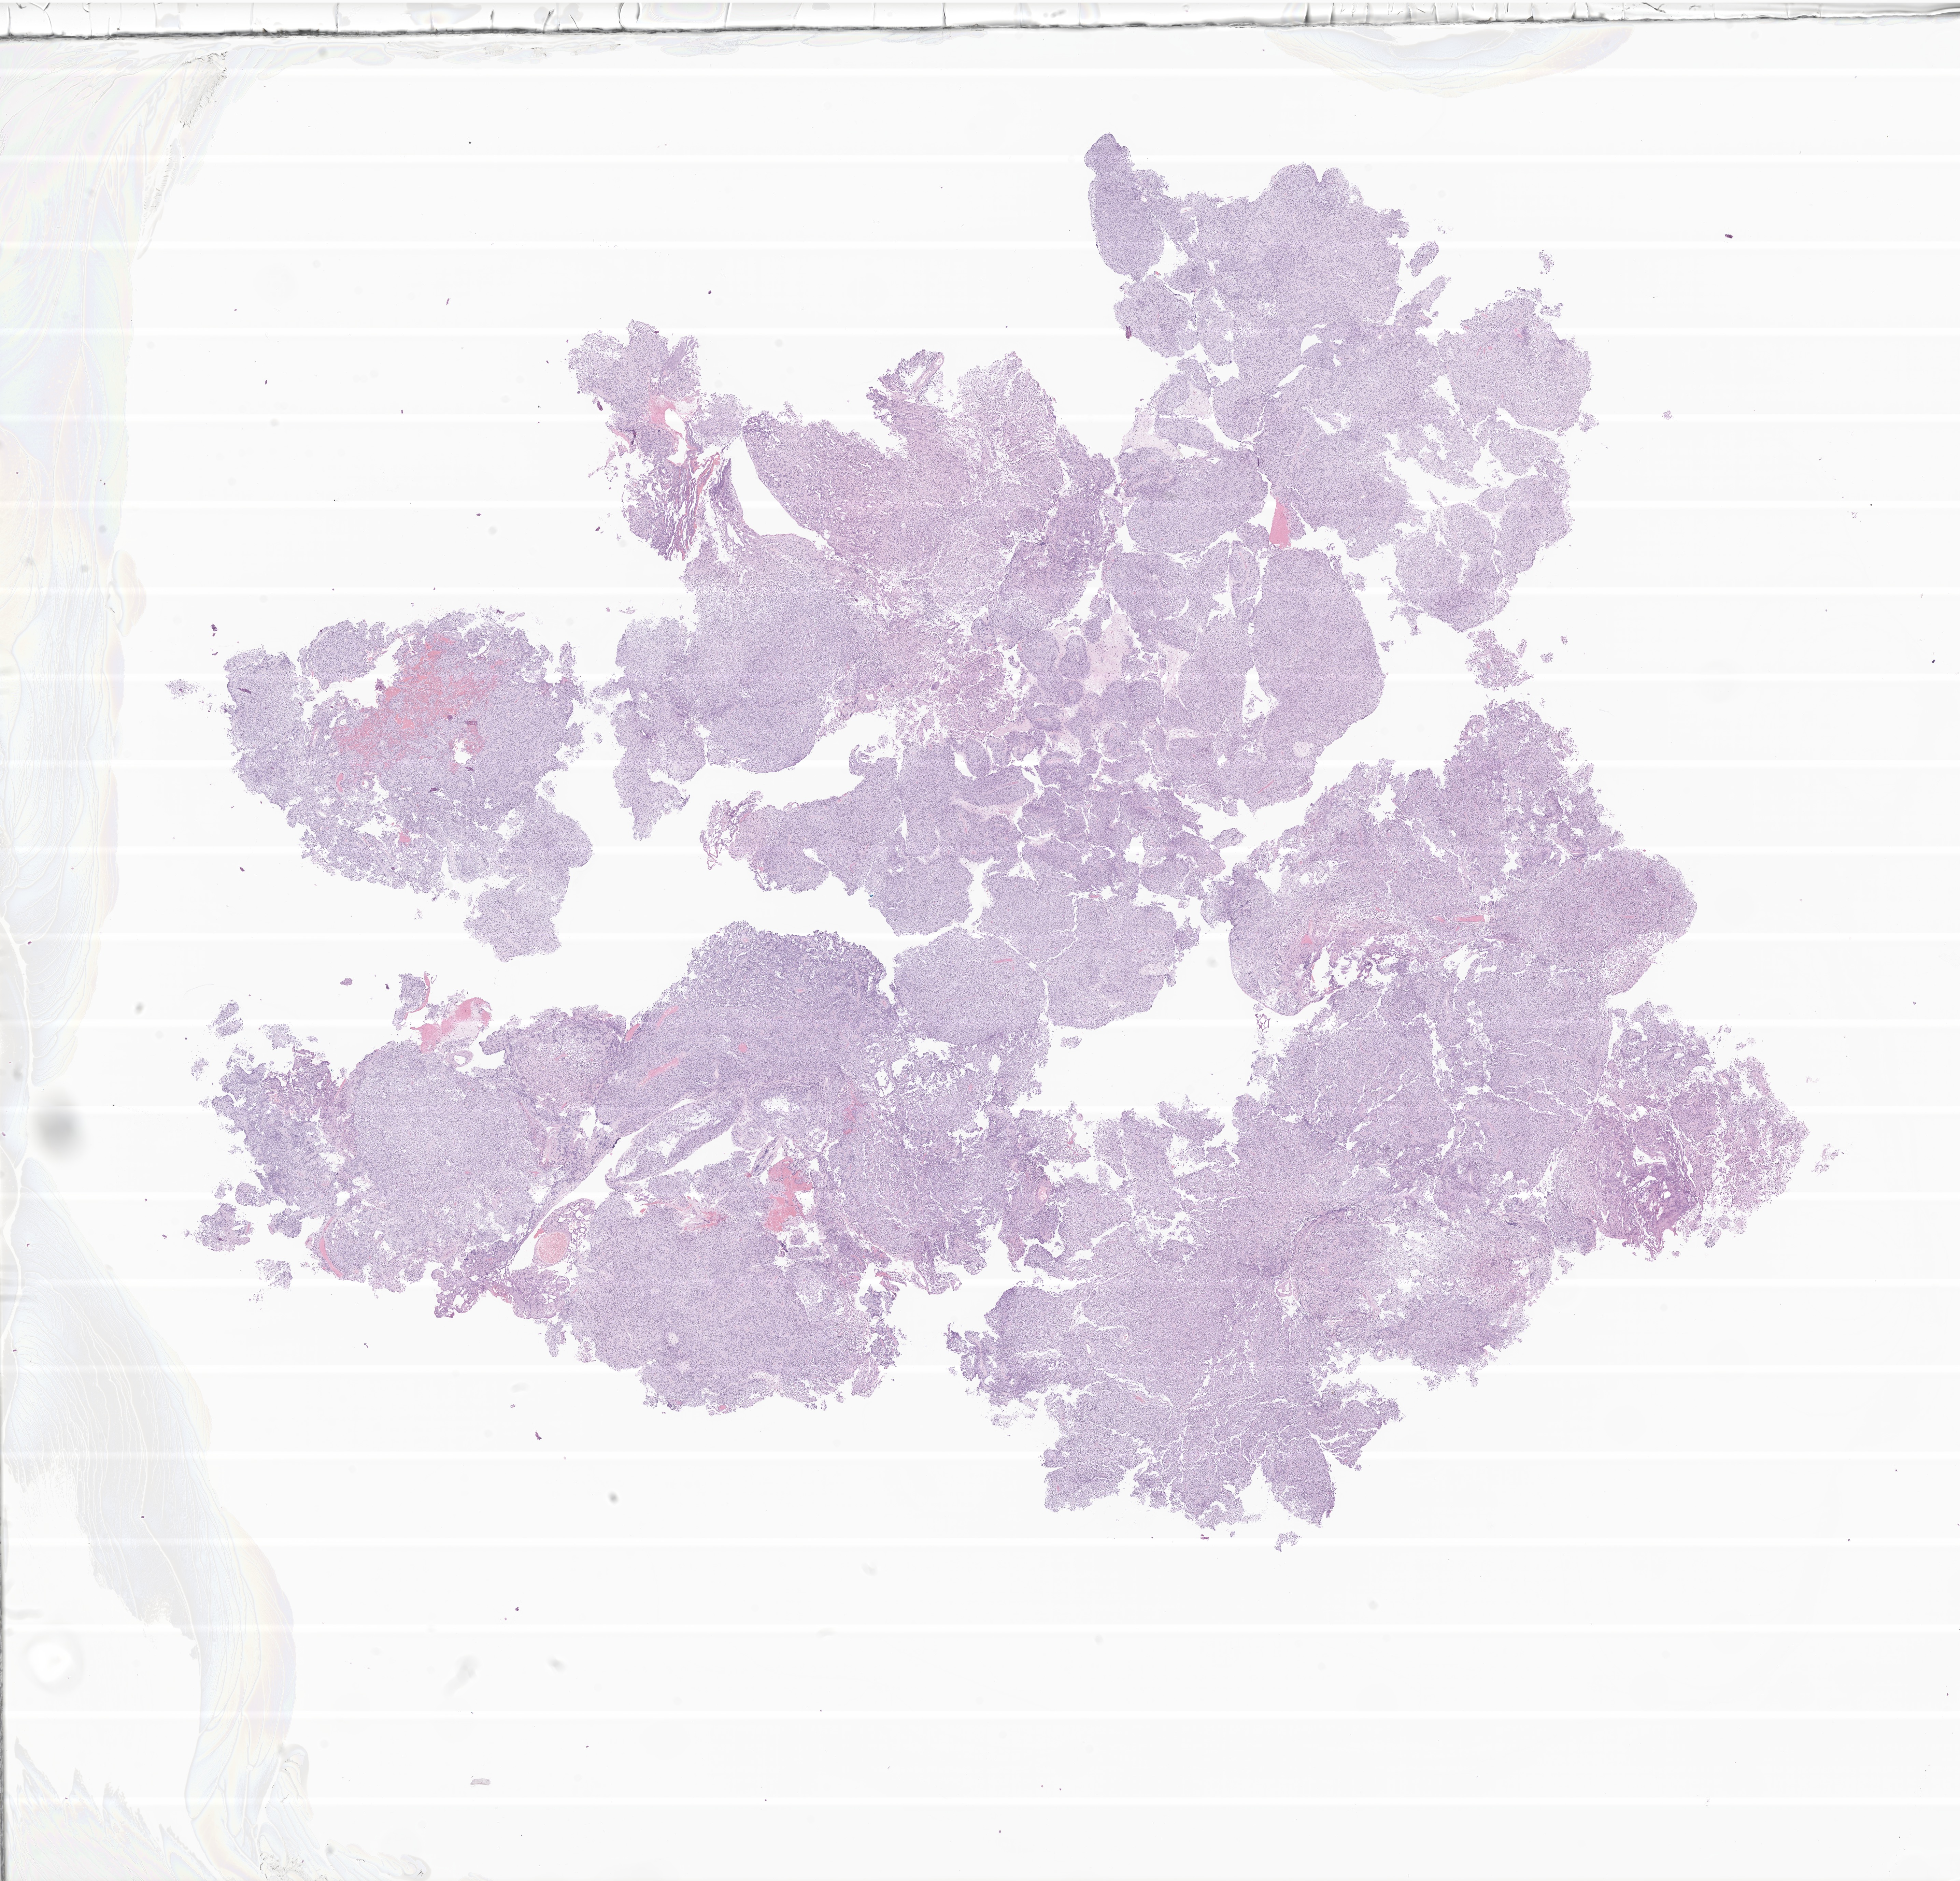
Hematoxylin and eosin (H&E) whole-slide image of tumor tissue from the brain — shown as a low-resolution overview of the whole scanned area (about 24.2 x 23.2 mm). Formalin-fixed, paraffin-embedded (FFPE) tissue. Patient: female, age 207 months (17 years 3 months).
Diagnosis: Neoplasm, uncertain whether benign or malignant.